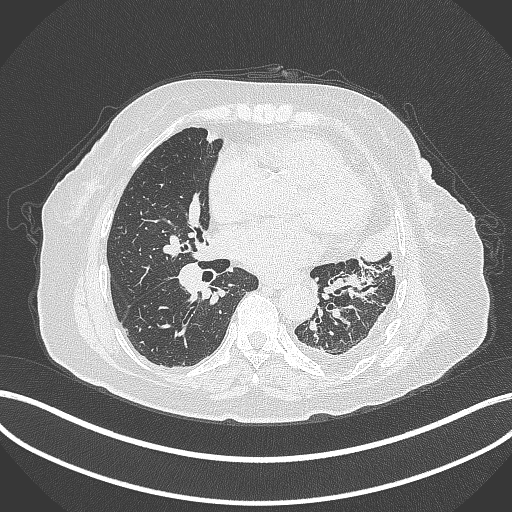
Chest CT, one axial slice; position 170 of 399 along the scan axis; reconstruction kernel B70f; 120 kVp; lung window (W 1500 / L -600 HU); 1 mm slice thickness; 512 × 512 image matrix, field of view 400 × 400 mm. Female patient, age 75 years. From the clinical record (not read from this slice): clinical TNM (as recorded): T3 N3 M1.
Structures marked on this image (rectangle marked by the reading radiologist):
- lung tumour (recorded histology: adenocarcinoma): box from (x=362, y=224) to (x=403, y=274) px